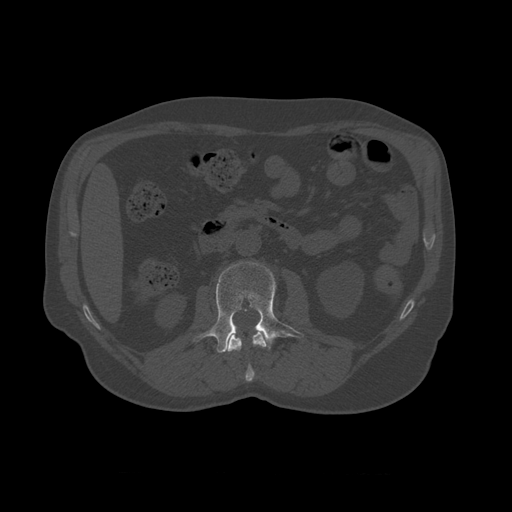
CT including the spine, one axial slice. Position 334 of 450 along the scan axis. 120 kVp. Bone window (W 1800 / L 400 HU). 1.25 mm slice thickness. 512 × 512 image matrix, field of view 405 × 405 mm. Patient age 75 years. From the clinical record (not read from this slice): primary cancer: prostate.
Annotated regions visible in this slice (semi-automatically segmented with operator editing):
- L1 vertebra: bounding box <226,330,268,382> (left, top, right, bottom; pixels)
- L2 vertebra: <193,262,304,353>